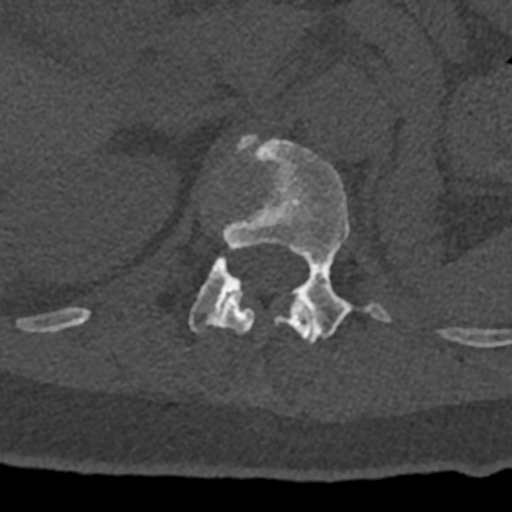
CT including the spine, one axial slice. Position 457 of 797 along the scan axis. 120 kVp. Bone window (W 1800 / L 400 HU). 512 × 512 image matrix, field of view 160 × 160 mm. Male patient, age 74 years. Case-level facts recorded for this patient, not image findings: primary cancer: renal; vertebrae with lytic lesions (as recorded): T10, L1, L2, L3, L4, L5.
Annotated regions visible in this slice (semi-automatically segmented with operator editing):
- L1 vertebra: box from (x=189, y=135) to (x=391, y=343) px
- T12 vertebra: (x=70, y=297)–(x=313, y=344)